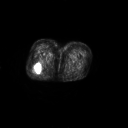
FDG PET of an extremity soft-tissue mass (from a PET/CT study), one axial slice. Slice 28 of 267 in the series (ordered by position). 3.27 mm slice thickness. 128 × 128 image matrix. Patient: female, 70 years. From the clinical record (not read from this slice): histological type: synovial sarcoma; grade: intermediate; site of the primary tumour: right buttock.
Annotated regions visible in this slice (expert contour drawn on MRI and transferred to this co-registered scan by the dataset authors):
- gross tumour volume including surrounding oedema: bounding box (x1, y1, x2, y2) in pixels: (34, 61, 41, 72)
- gross tumour volume (mass): (34, 64, 40, 72)